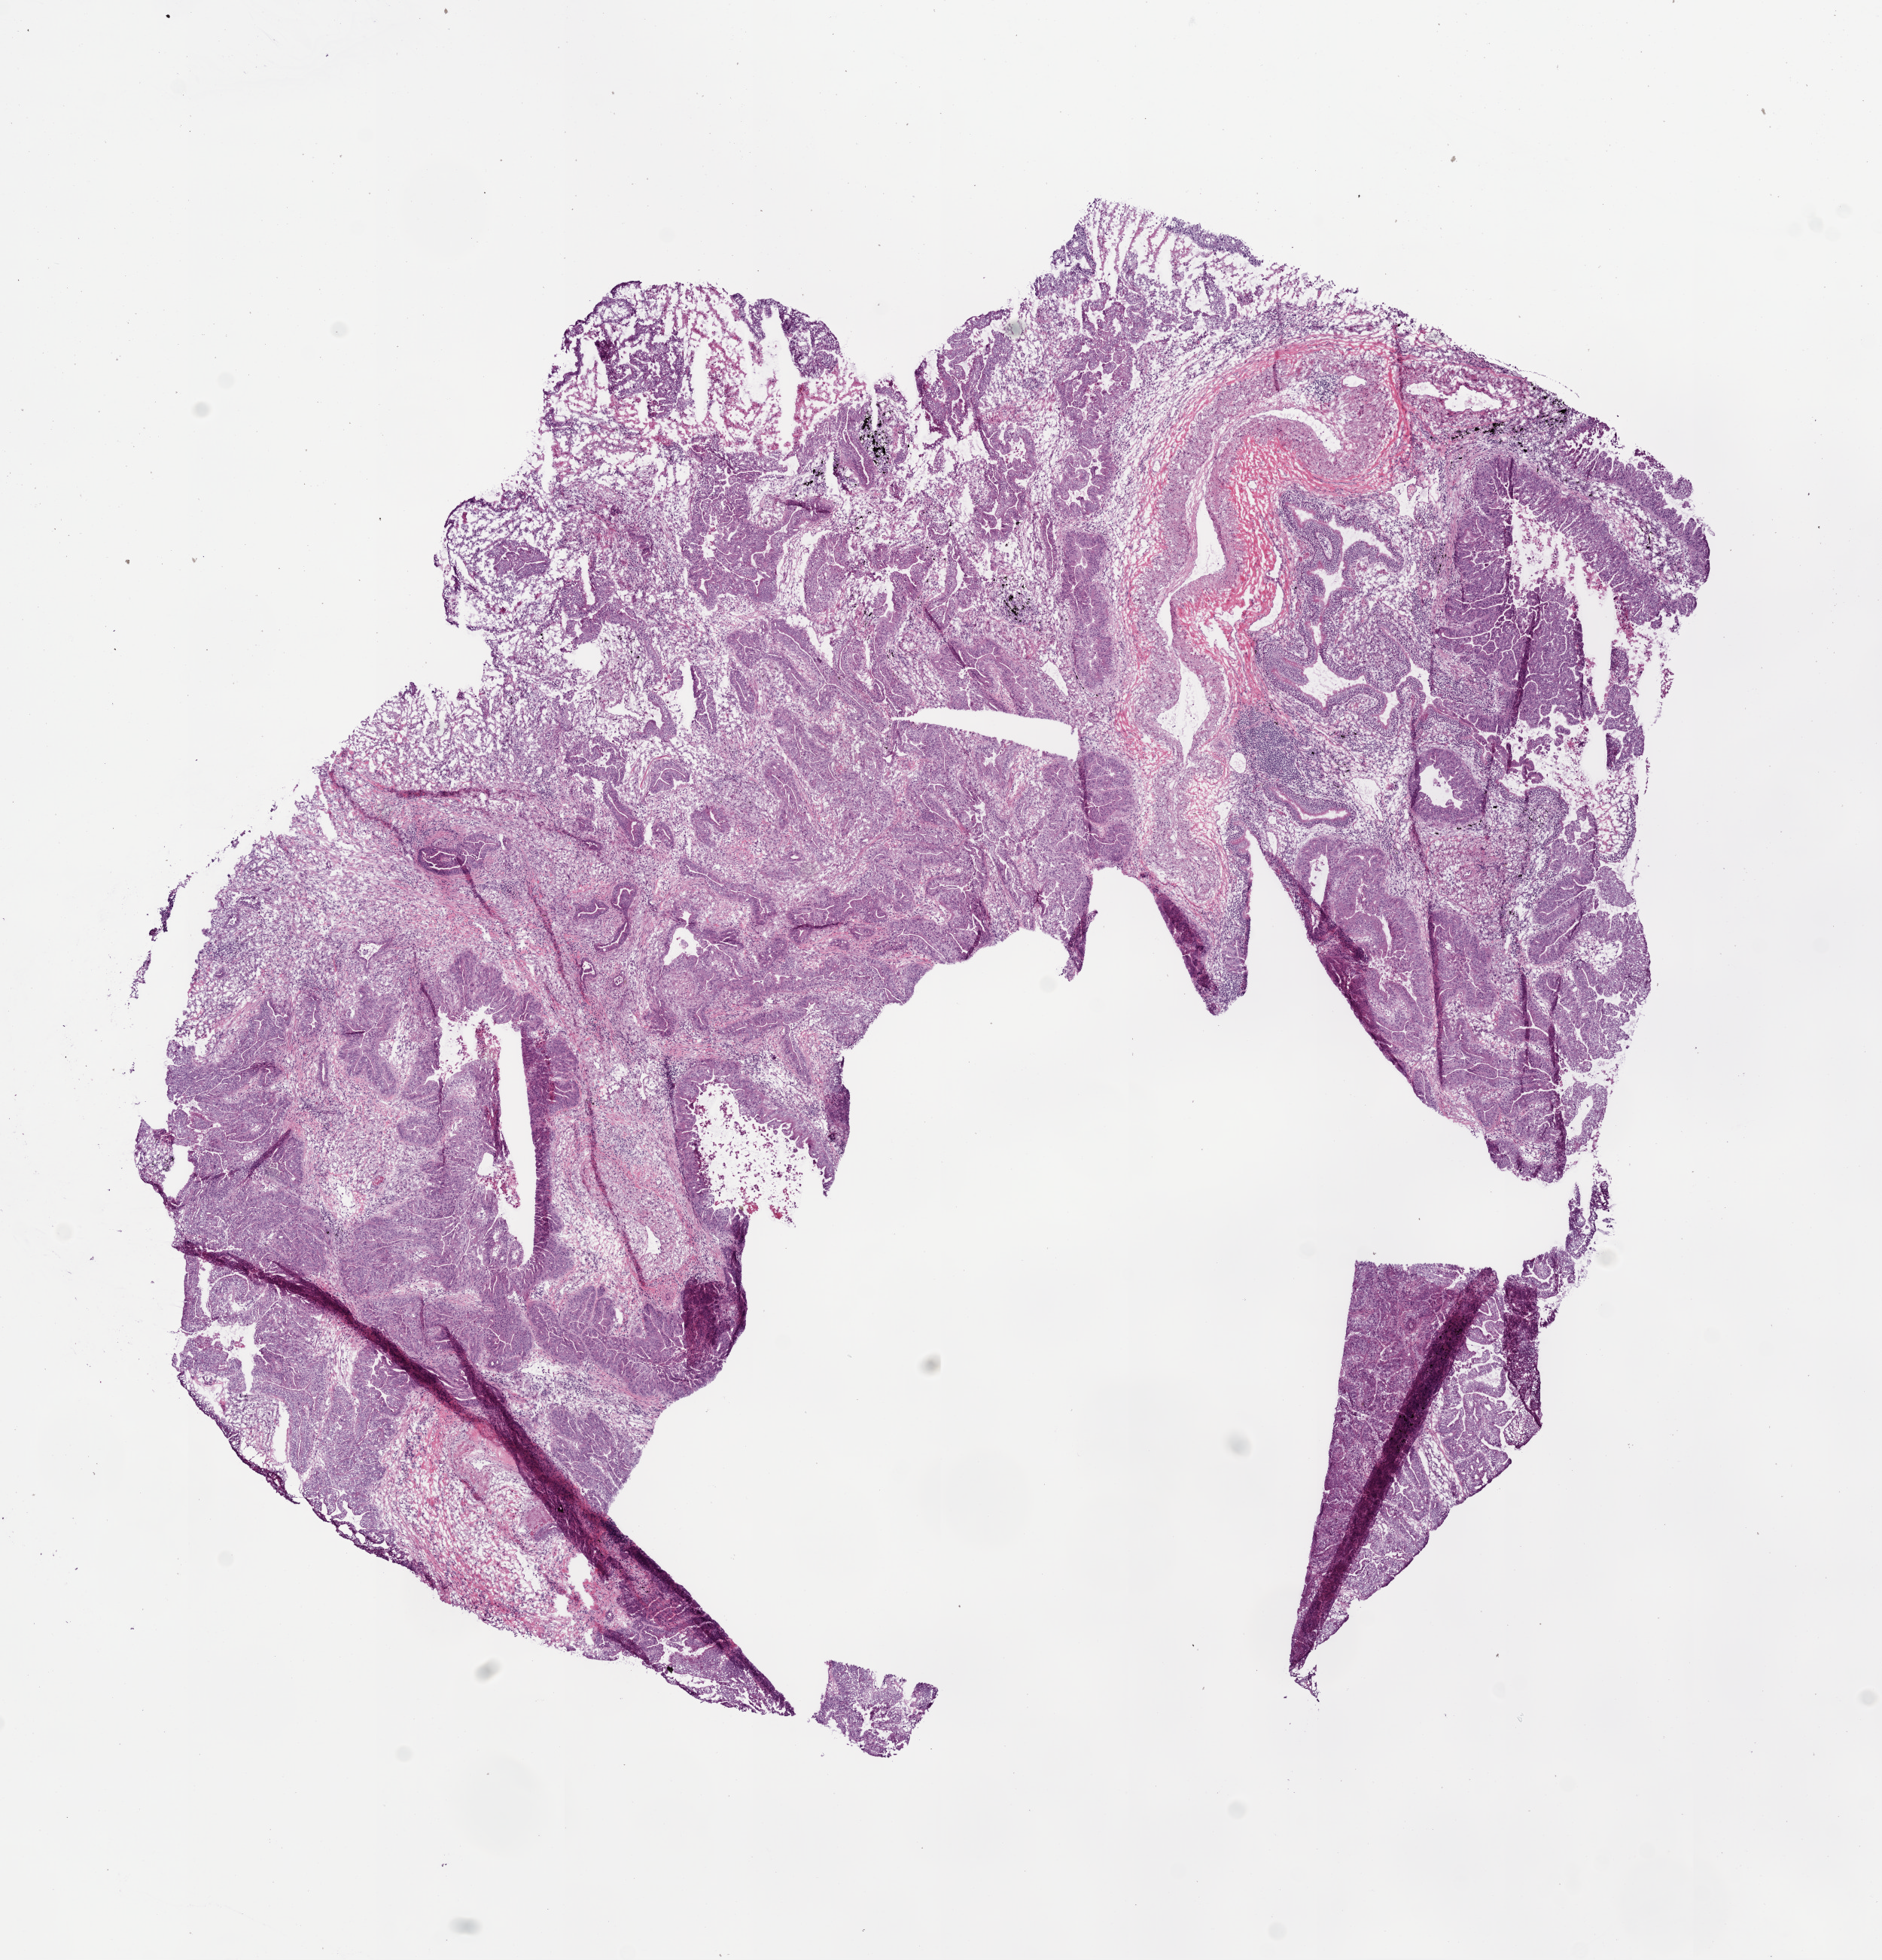
H&E whole-slide image — a low-resolution overview of the entire scanned area, about 10.0 x 10.4 mm (slide scanned at 20x); frozen section from the bottom of the tissue portion; sample: primary tumour, lung. Male patient; age at initial diagnosis 60 years. Composition of this section per pathologist review: tumour cells 90%, tumour nuclei 80%, normal cells 0%, stromal cells 10%, necrosis 0%. Inflammatory infiltration, as recorded: lymphocyte infiltration 5%, monocyte infiltration 1%, neutrophil infiltration 5%.
Diagnosis: Adenocarcinoma, NOS. AJCC pathologic stage: IIIA (7th edition).